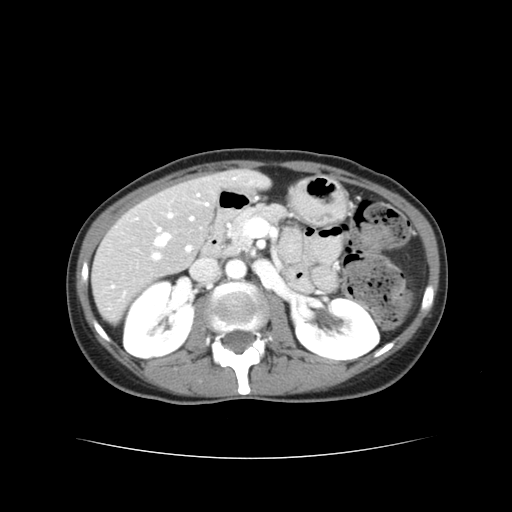
Contrast-enhanced abdominal CT, one axial slice; slice 17 of 38 in the series (ordered by position); reconstruction kernel STANDARD; 120 kVp; intravenous contrast given; soft-tissue window (W 400 / L 40 HU); 5 mm slice thickness; 512 × 512 image matrix, field of view 340 × 340 mm. Female patient, age 54 years. From the clinical record (not read from this slice): diagnosis: colorectal cancer liver metastases, imaged before liver resection; multiple liver metastases: yes; largest metastasis: 1.1 cm.
Outlined on this slice (outlined manually by an expert reader):
- hepatic veins: box from (x=156, y=204) to (x=208, y=246) px
- liver: (x=93, y=171)–(x=265, y=319)
- planned liver remnant (the part of the liver to remain after resection): (x=221, y=171)–(x=265, y=187)
- portal vein (with intrahepatic branches): (x=154, y=215)–(x=194, y=259)